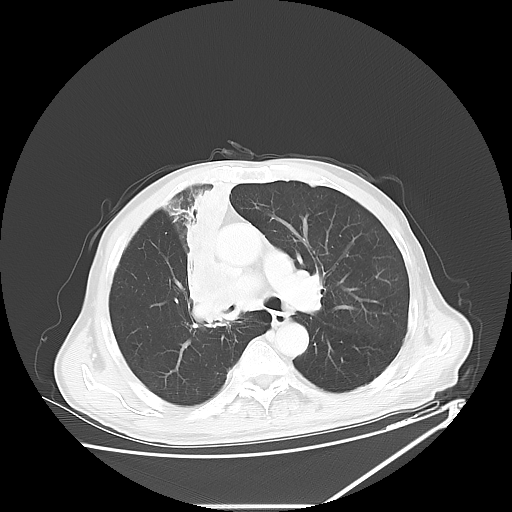
Chest CT, one axial slice. Slice 39 of 60 in the series (ordered by position). 120 kVp. Lung window (W 1500 / L -600 HU). 5 mm slice thickness. 512 × 512 image matrix. Male patient, age 73 years. From the clinical record (not read from this slice): clinical TNM (as recorded): T2a N1 M0.
Annotated regions visible in this slice (bounding box drawn by a radiologist):
- lung tumour (recorded histology: squamous cell carcinoma): box from (x=167, y=171) to (x=255, y=335) px